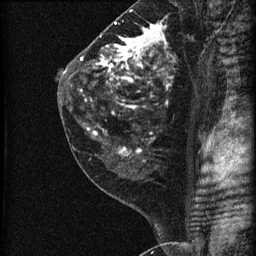
Breast MRI (dynamic contrast-enhanced), one sagittal slice; position 32 of 60 along the scan axis; dynamic contrast-enhanced series, image 2 of 3 at this slice position (ordered by acquisition); 1.5 T; TE 4.2 ms, TR 22.7 ms; 1.8 mm slice thickness; 256 × 256 image matrix, field of view 180 × 180 mm. Patient: female, 45 years. From the clinical record (not read from this slice): setting: breast cancer imaged before/during neoadjuvant chemotherapy; receptor status: HR-positive, HER2-negative.
Annotated regions visible in this slice (semi-automatically segmented with operator editing):
- analysis volume of interest (the breast-tissue region the enhancement analysis was run in; not a lesion): box from (x=74, y=11) to (x=205, y=140) px
- tumour enhancement mask (voxels above the 90 % enhancement threshold inside the analysis volume of interest): (x=80, y=22)–(x=172, y=134)